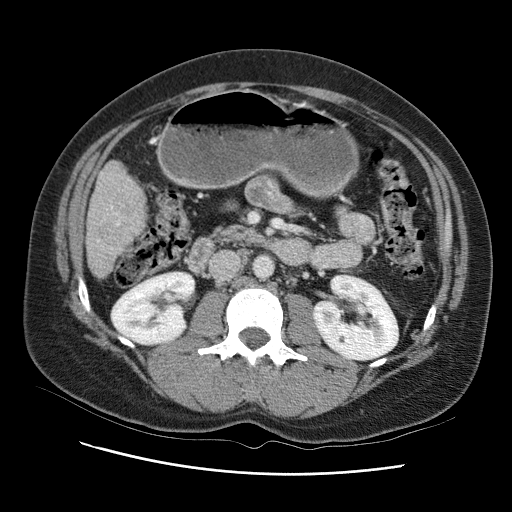
Contrast-enhanced abdominal CT (liver protocol), one axial slice. Slice 28 of 95 in the series (ordered by position). One of 2 acquisitions stored at this slice position. Soft-tissue window (W 400 / L 40 HU). 2.5 mm slice thickness. 512 × 512 image matrix, field of view 360 × 360 mm. From the clinical record (not read from this slice): diagnosis: hepatocellular carcinoma (patient treated with transarterial chemoembolisation; whether this scan precedes or follows treatment is not stated here); TNM stage (as recorded): Stage-I; Child-Pugh class: B; tumour differentiation: moderately differentiated; tumour nodularity: uninodular.
Outlined on this slice (semi-automatic segmentation, software-assisted and operator-edited):
- liver parenchyma outside the tumour (the mass and vessels are separate outlines, so this box may not span the whole liver): bounding box <86,148,160,276> (left, top, right, bottom; pixels)
- liver vessels: <102,198,134,254>